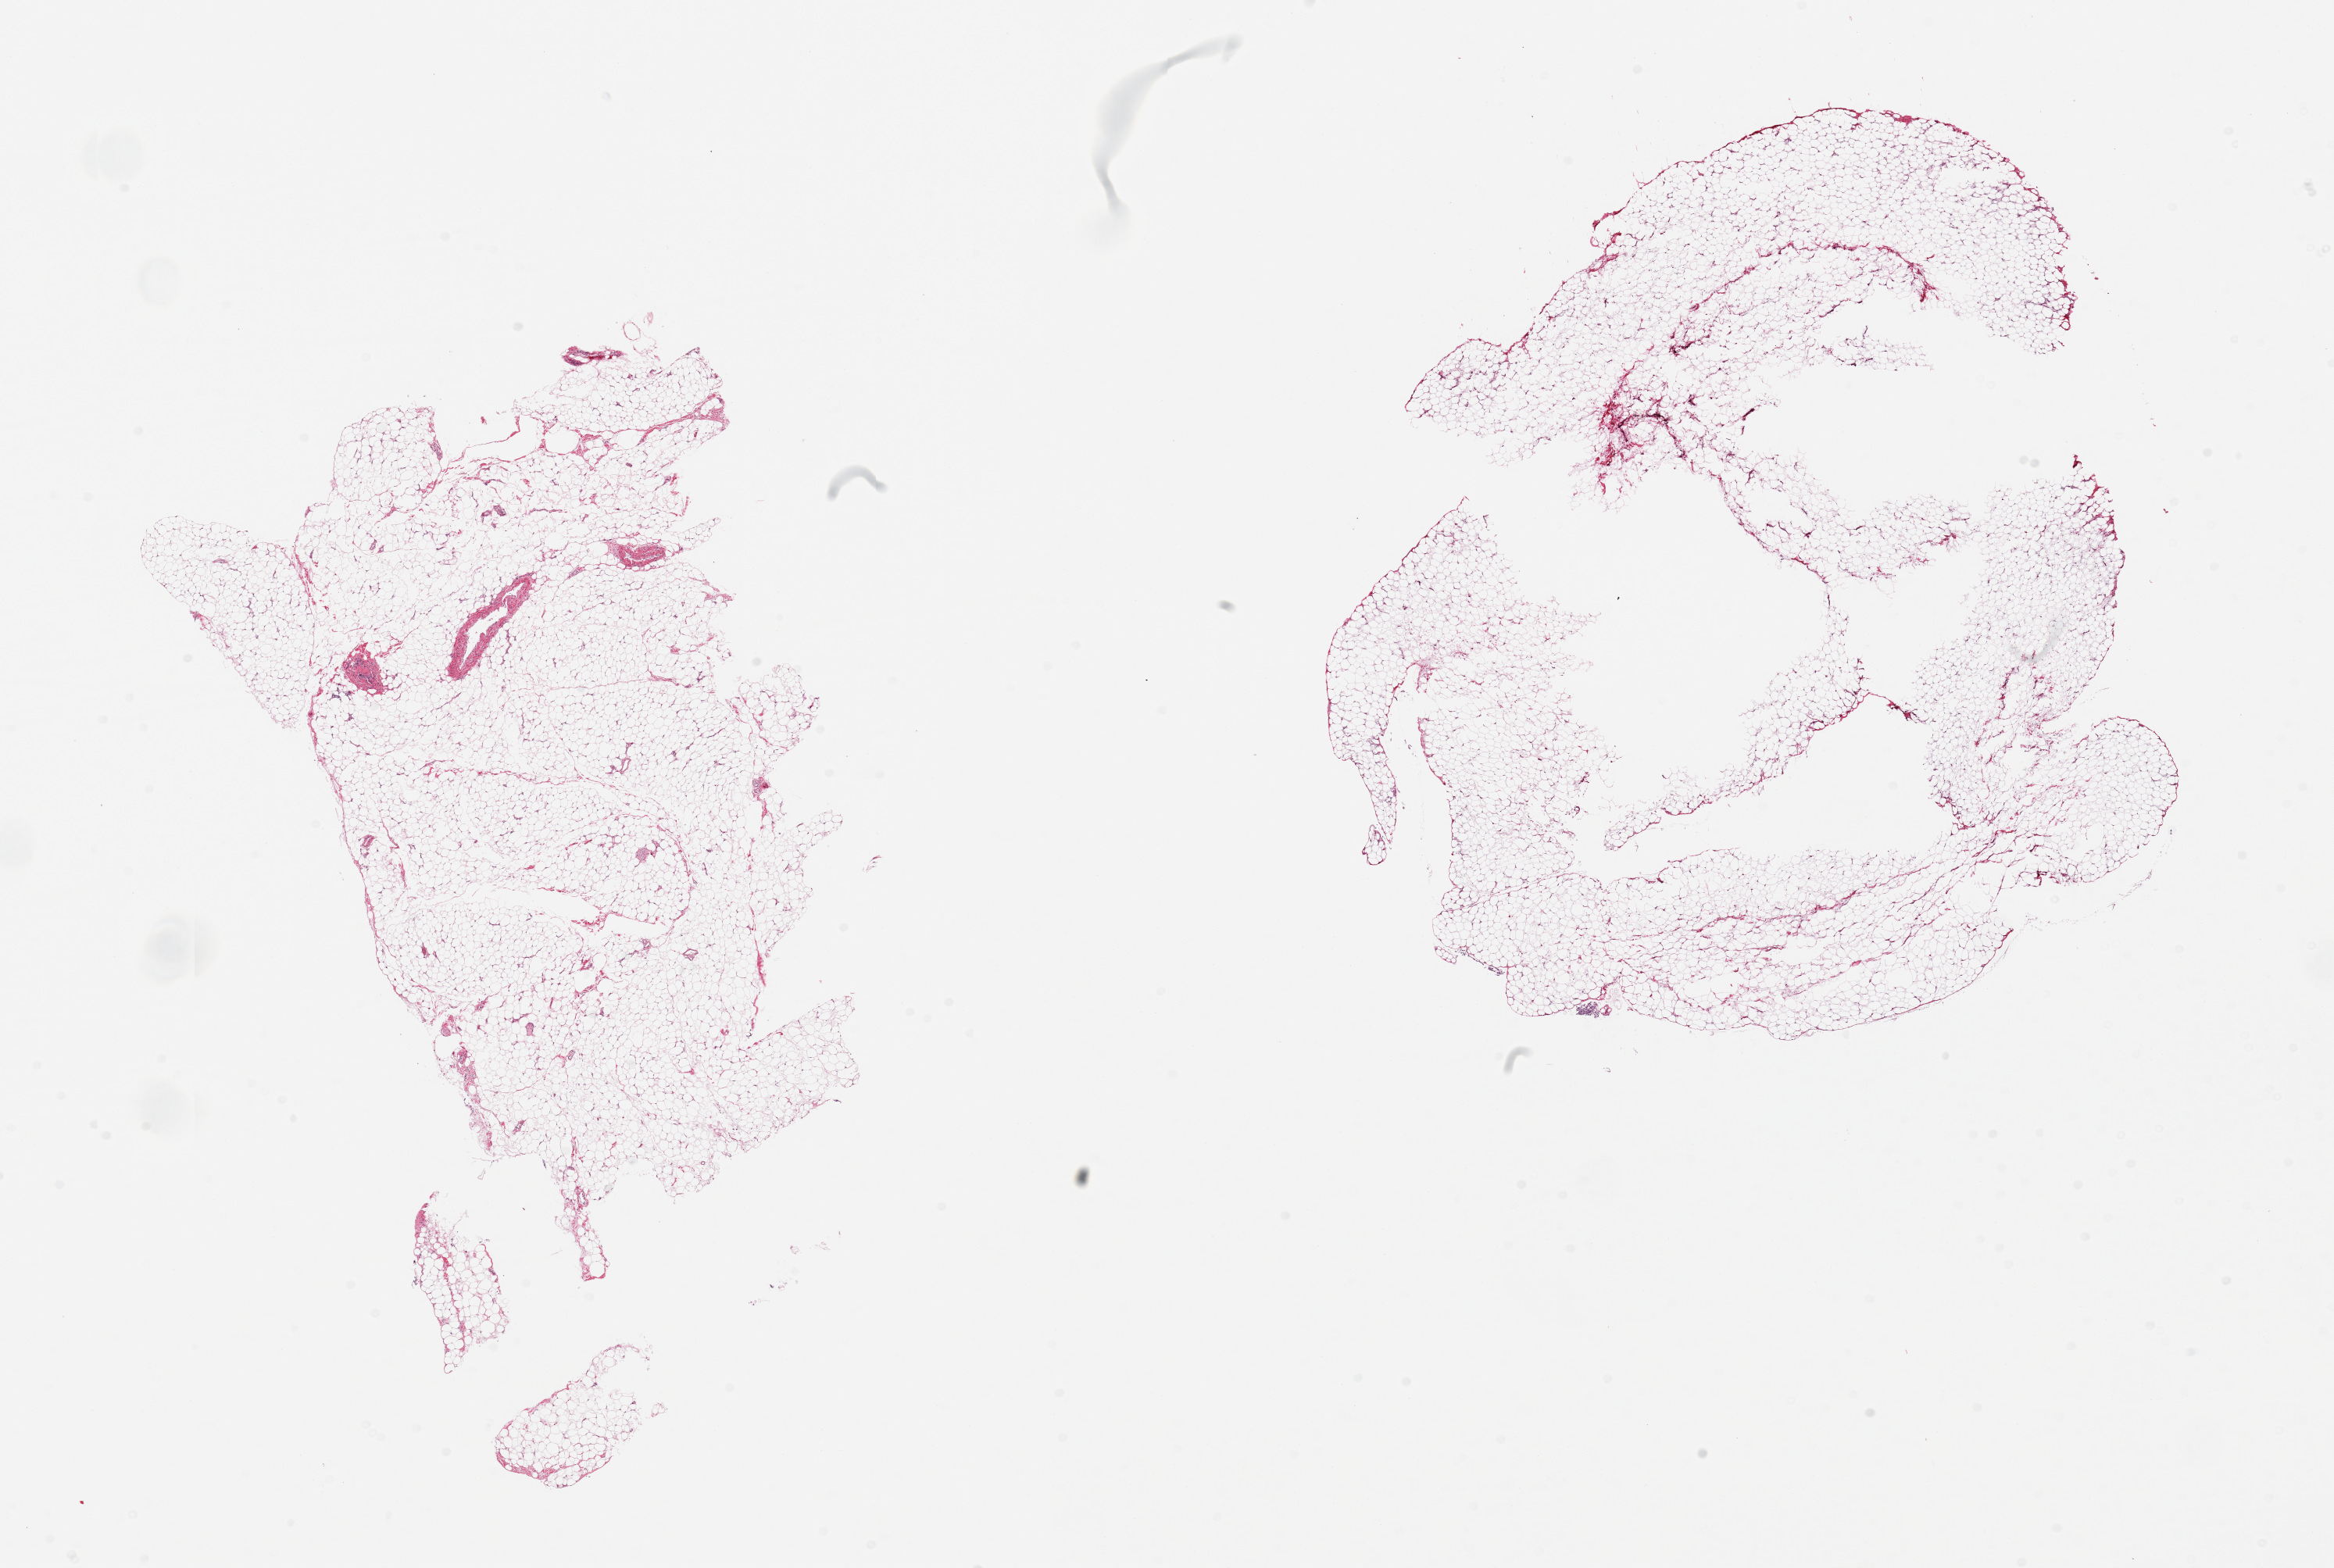
Whole-slide image, H&E stain, brightfield, low-resolution overview of the scanned area, about 23.6 x 15.9 mm (from a 20x scan), PAXgene-fixed paraffin-embedded (PFPE) section, target tissue: omentum, donor tissue sample. Male donor.
Pathologist's review note for this sample: 2 pieces; large central defects (? poor fixation).